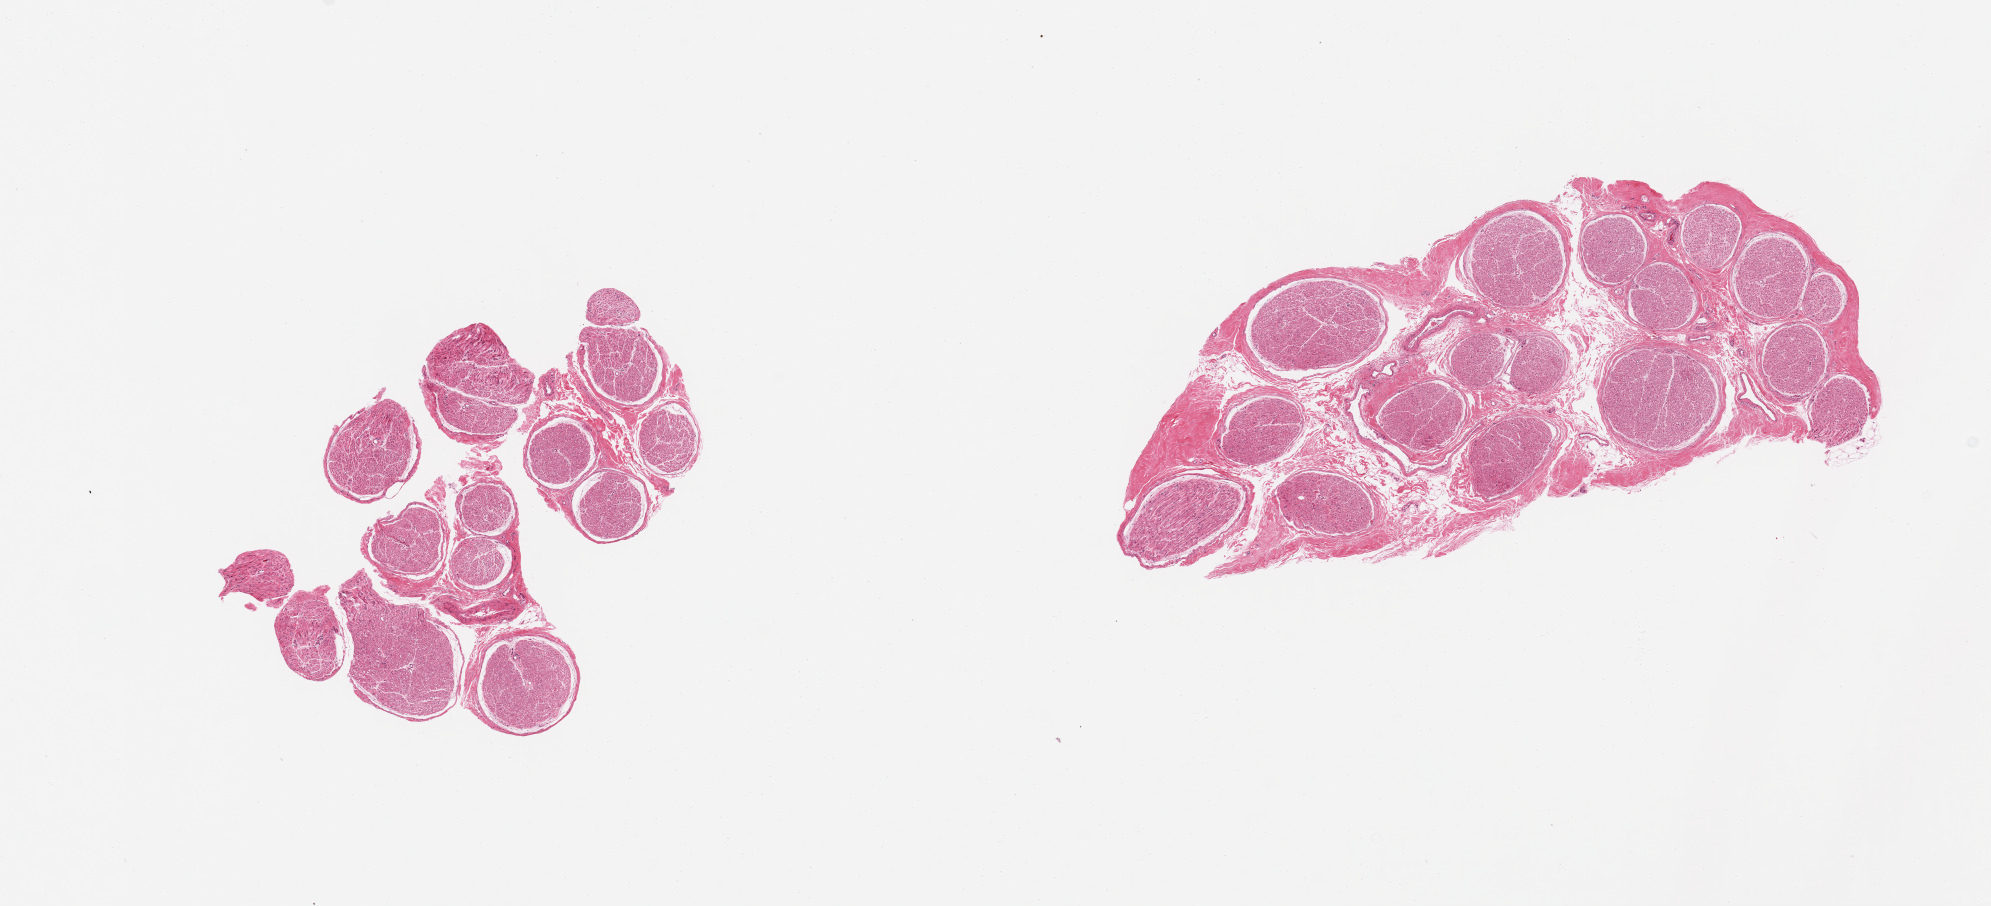
Hematoxylin and eosin (H&E) whole-slide image, brightfield — a low-resolution overview of the entire scanned area, about 15.8 x 7.2 mm (acquisition: 20x scan), PAXgene-fixed paraffin-embedded (PFPE) section, target tissue: tibial nerve, tissue donor sample.
• reviewer comment on this tissue sample: 2 pieces; <5% fat content